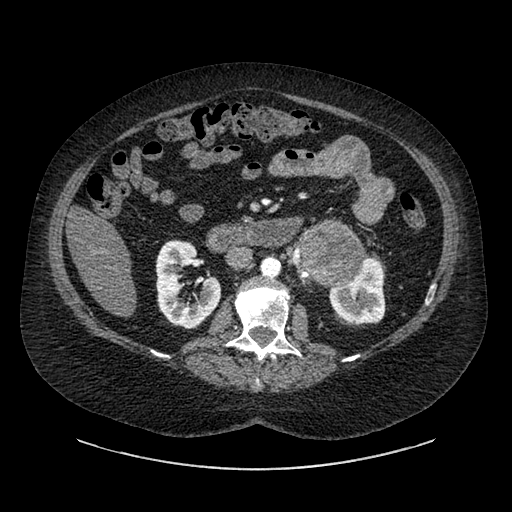
Contrast-enhanced abdominal CT, one axial slice. Position 506 of 769 along the scan axis. Reconstruction kernel SOFT. 120 kVp. Soft-tissue window (W 400 / L 40 HU). 512 × 512 image matrix. Patient: female, 61 years. From the clinical record (not read from this slice): diagnosis: adrenocortical carcinoma; tumour side: left adrenal; tumour size at pathology: 13 cm; Ki-67 index: 79 %; stage (as recorded): 2.
Outlined on this slice (semi-automatically segmented with operator editing):
- mass: box from (x=299, y=226) to (x=363, y=281) px